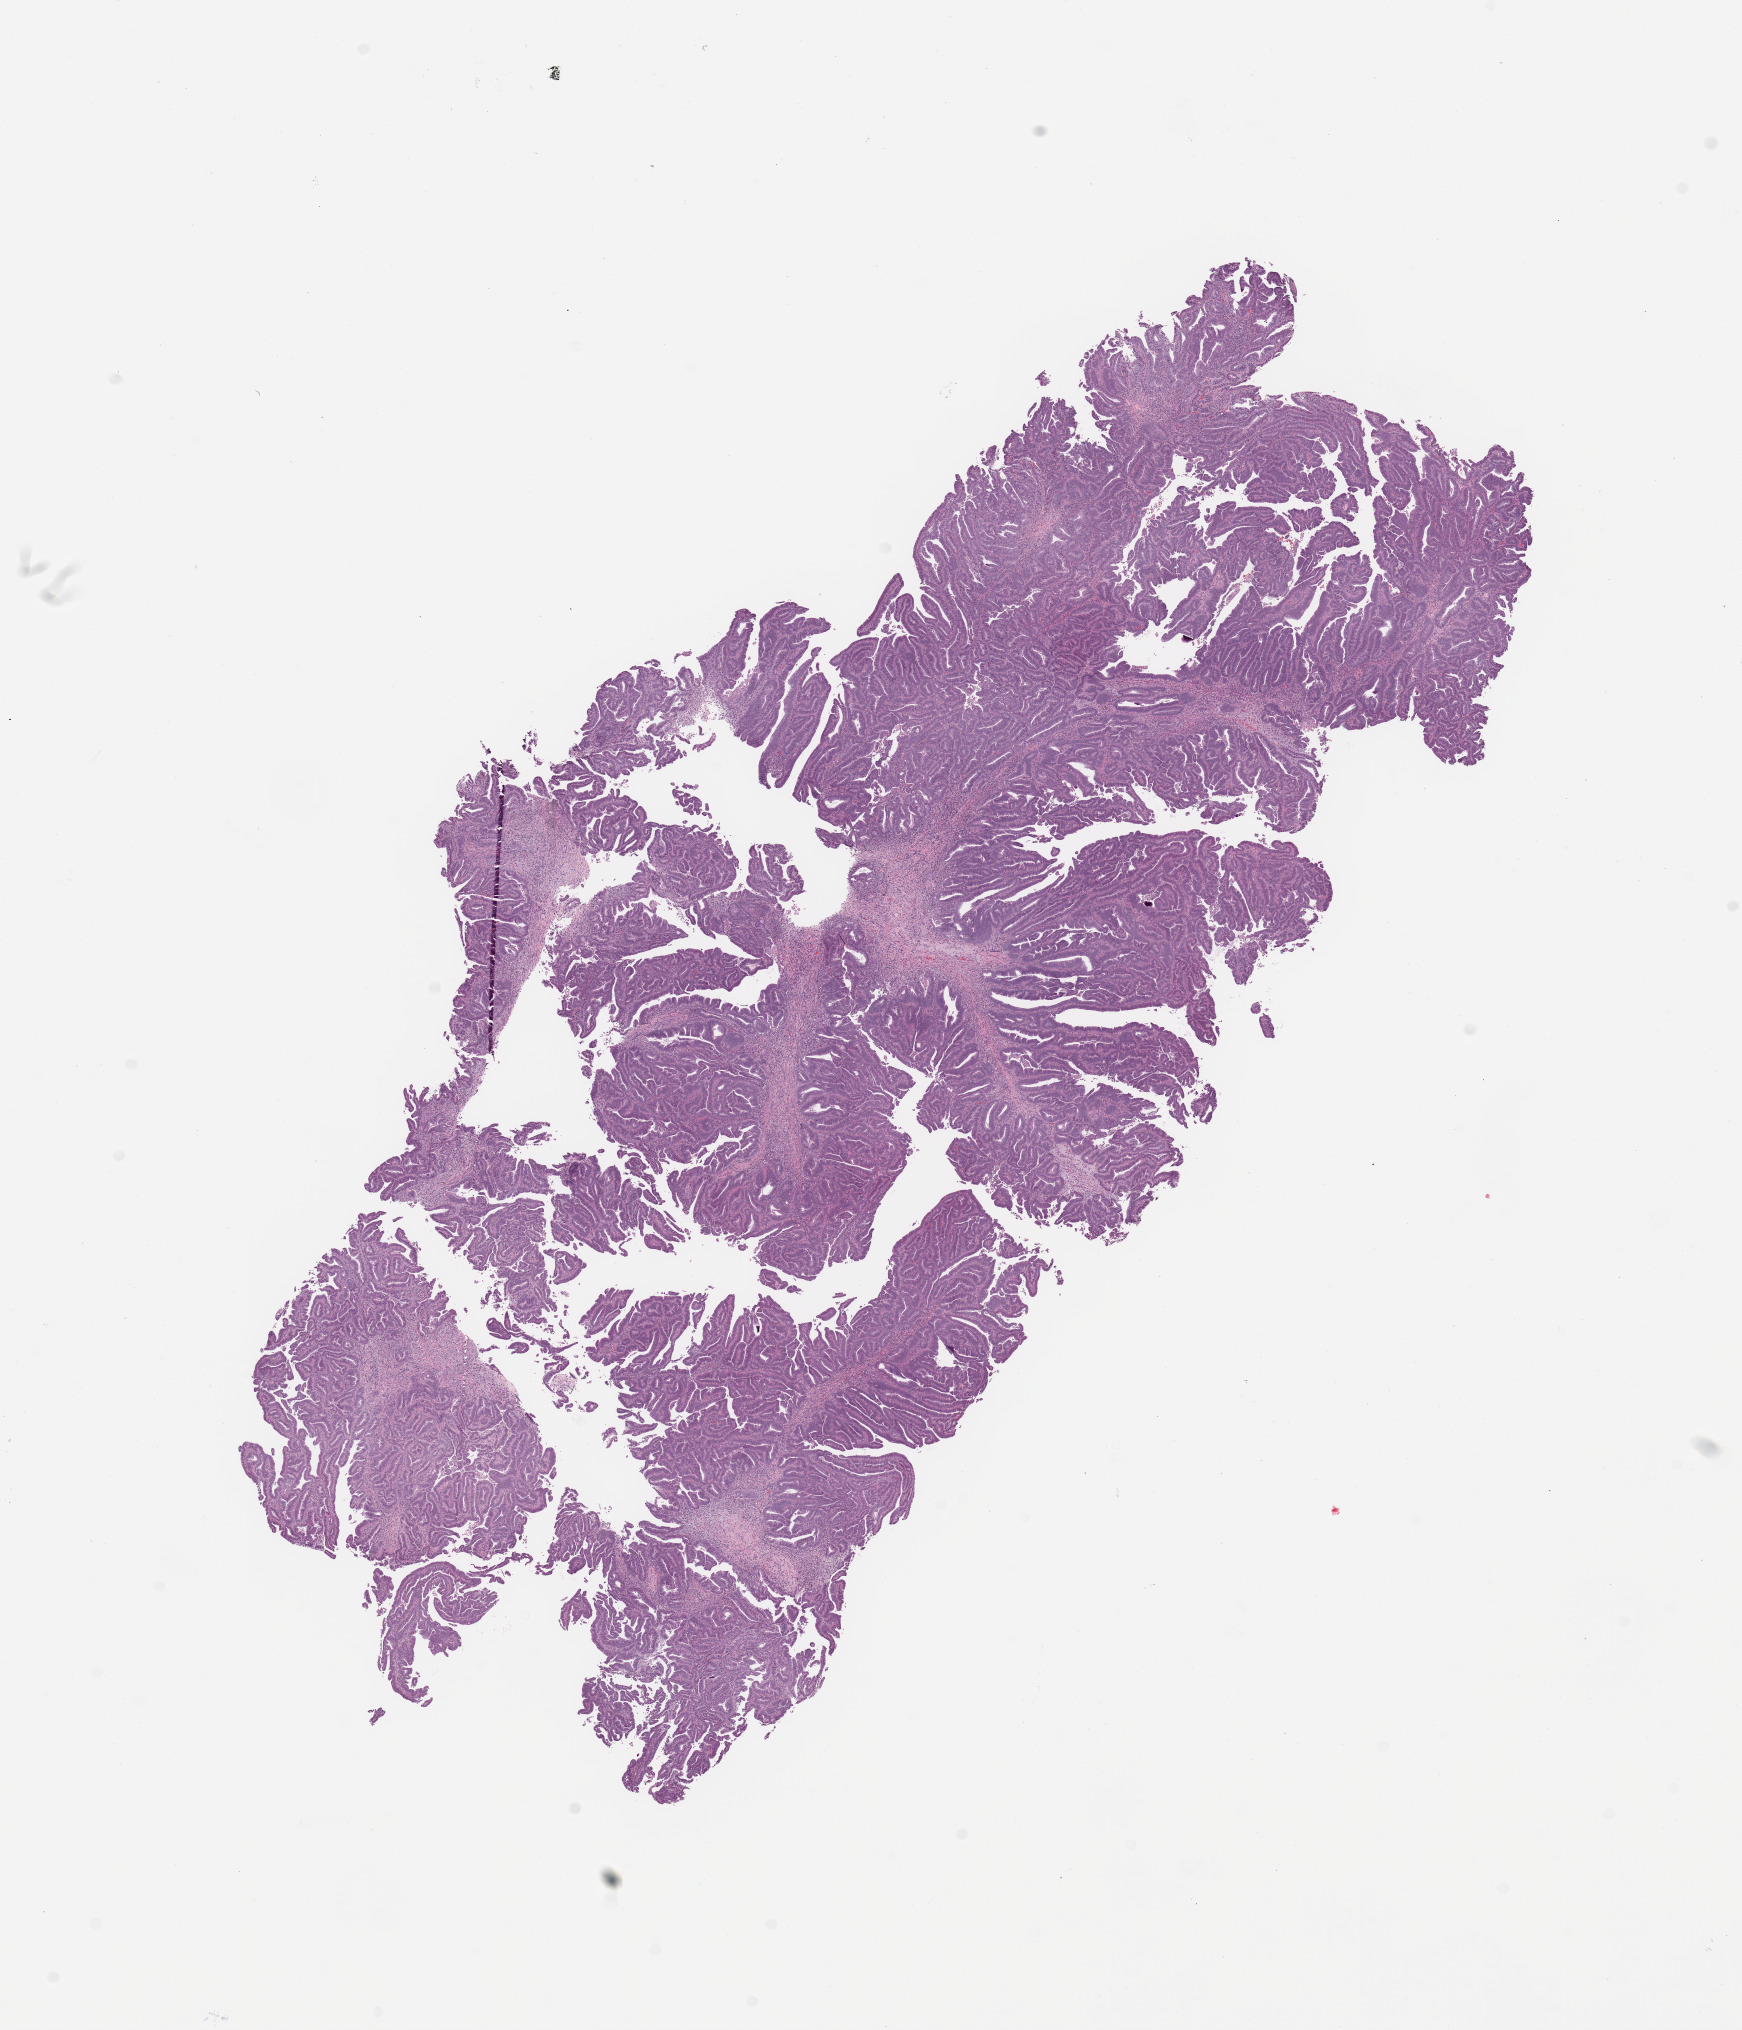
Whole-slide histology image, Hematoxylin and eosin (H&E) stained — shown as a low-resolution overview of the whole scanned area (about 13.8 x 16.1 mm), tumour tissue sample, sampled site: uterus. Patient: female, age 64 years. Composition of this section per pathologist review: tumour nuclei 80%, necrosis 0%.
Diagnosis: Endometrioid adenocarcinoma, NOS.